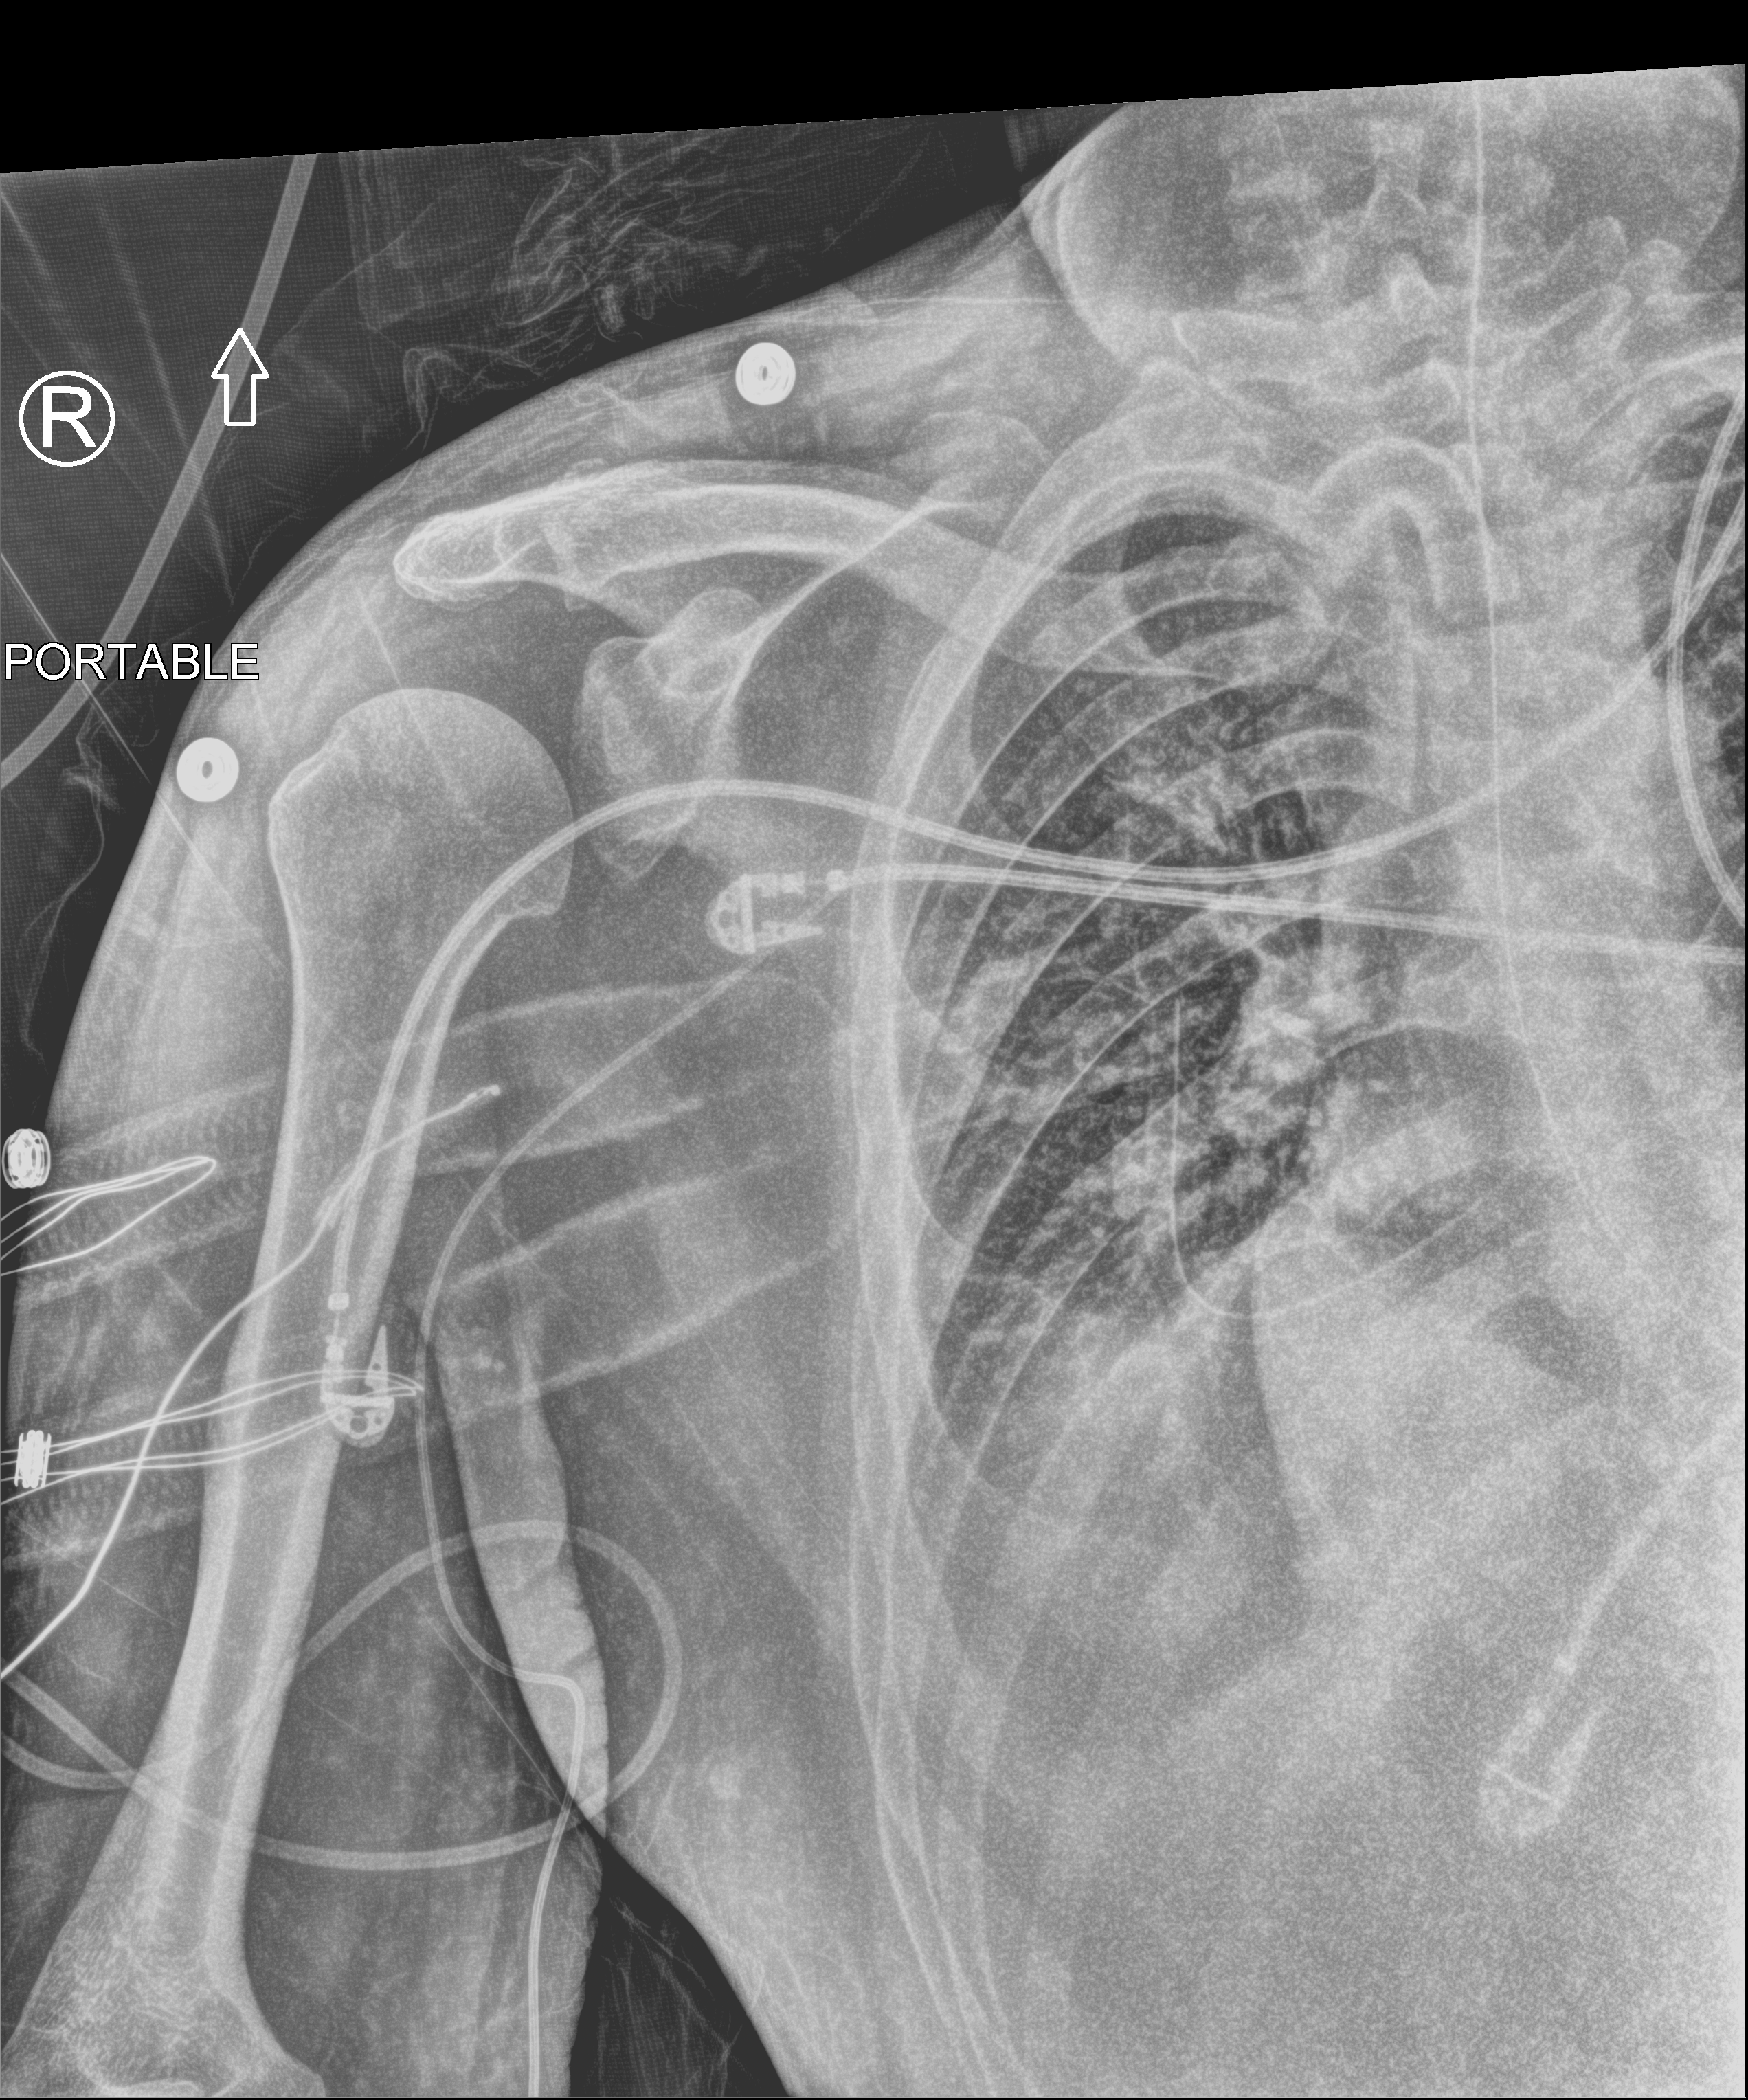
Portable chest radiograph, anteroposterior (AP) projection. Male patient hospitalised with COVID-19, age 18–59 years.
Hospital-stay facts (about this admission, not read from this image; timing relative to this image not recorded): mechanically ventilated during this hospital stay: yes; length of hospital stay: 65 days.